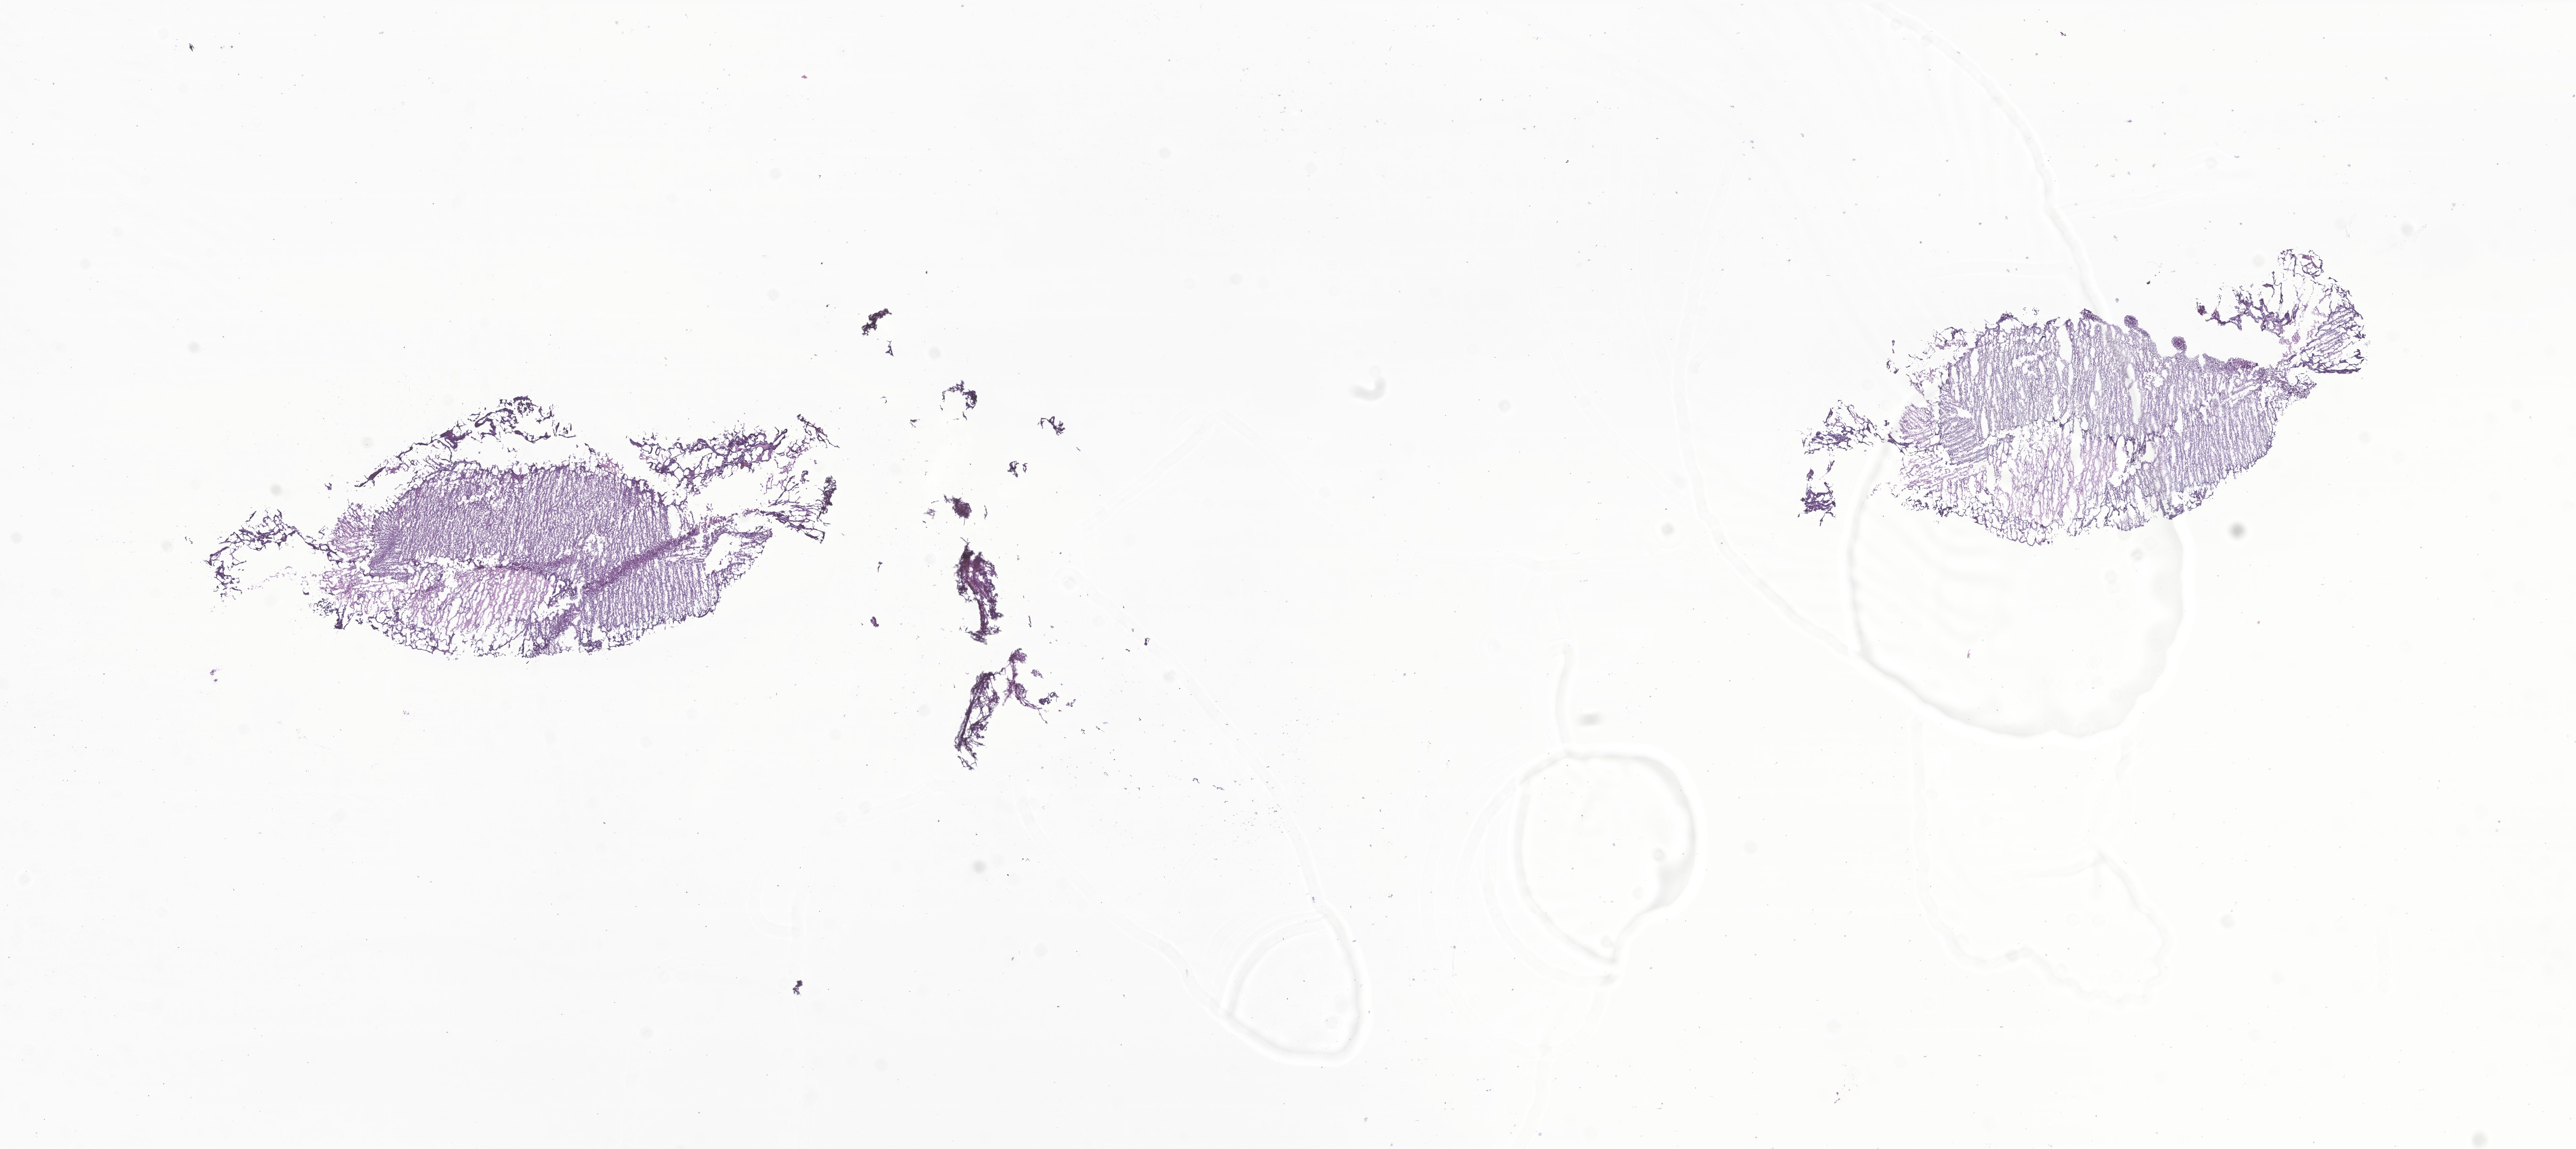
Digitized haematoxylin and eosin-stained section of tumor tissue from the brain, low-resolution overview of the scanned area, about 23.1 x 10.3 mm, frozen section. Female patient, age 130 months (10 years 10 months).
* recorded diagnosis: Malignant tumor, small cell type